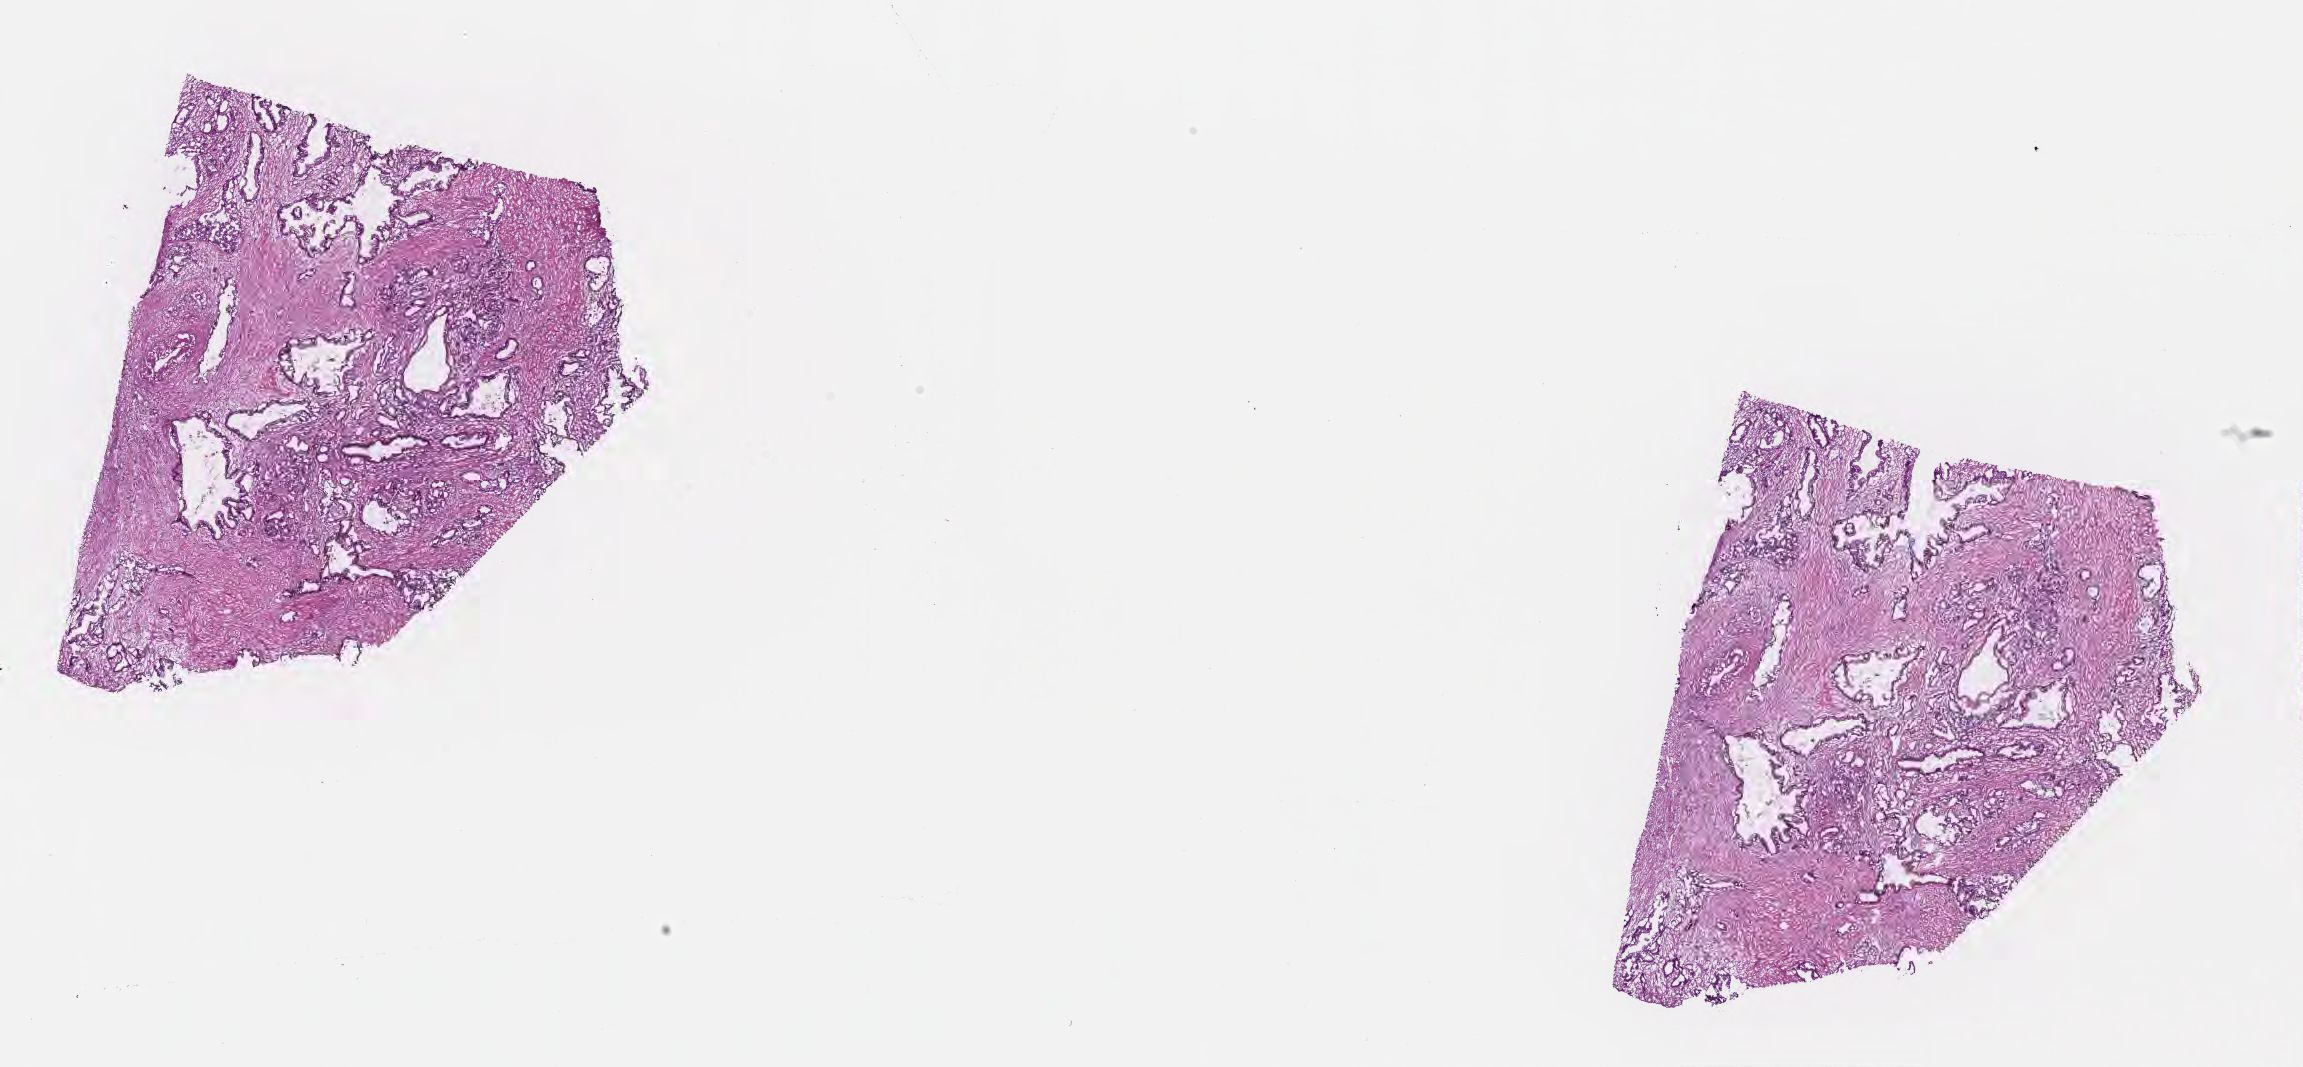
Haematoxylin and eosin whole-slide image — a low-resolution overview of the entire scanned area, about 18.6 x 8.6 mm. Frozen section. Primary tumor. Anatomic site: tail of pancreas. Female patient; age at initial diagnosis 74 years. Tumor grade: G2 (moderately differentiated). Pathologist review of this section (percent, as recorded): tumor cells 20%, tumor nuclei 20%, stromal cells 40%, necrosis 0%, normal cells 40%. Infiltration values recorded for this section: lymphocyte infiltration 10%, monocyte infiltration 7%, neutrophil infiltration 9%.
AJCC pathologic stage: Stage IIB. Diagnosis: Infiltrating duct carcinoma, NOS.